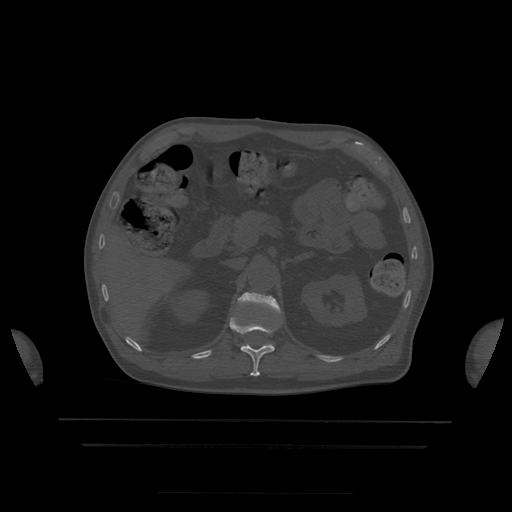
CT including the spine, one axial slice; position 187 of 522 along the scan axis; bone window (W 1800 / L 400 HU); 512 × 512 image matrix. Patient age 68 years. Case-level facts recorded for this patient, not image findings: primary cancer: urothelial.
Structures marked on this image (semi-automatic segmentation, software-assisted and operator-edited):
- L1 vertebra: bounding box (x1, y1, x2, y2) in pixels: (238, 293, 281, 315)
- T12 vertebra: (230, 317, 275, 377)